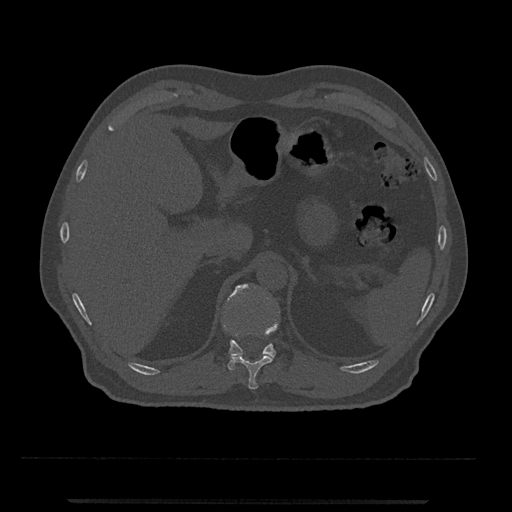
CT including the spine, one axial slice. Slice 436 of 797 in the series (ordered by position). Bone window (W 1800 / L 400 HU). 0.5 mm slice thickness. 512 × 512 image matrix, field of view 419 × 419 mm. Patient: male, 63 years. From the clinical record (not read from this slice): primary cancer: prostate.
Annotated regions visible in this slice (semi-automatic segmentation, software-assisted and operator-edited):
- T11 vertebra: bounding box <232,316,278,390> (left, top, right, bottom; pixels)
- T12 vertebra: <223,284,277,371>